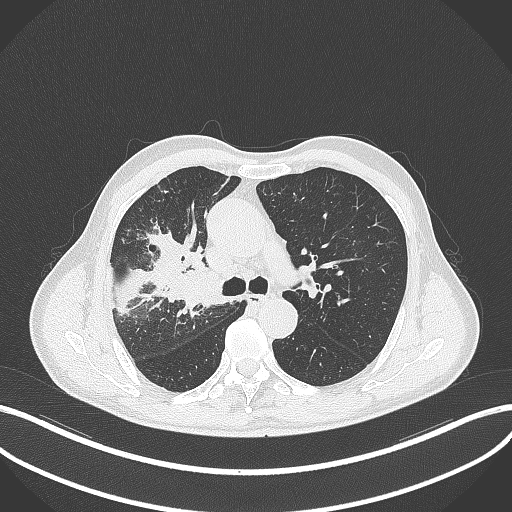
Chest CT, one axial slice. Position 321 of 490 along the scan axis. Reconstruction kernel B70f. 120 kVp. Lung window (W 1500 / L -600 HU). 1 mm slice thickness. 512 × 512 image matrix, field of view 400 × 400 mm. Male patient, age 69 years. From the clinical record (not read from this slice): clinical TNM (as recorded): T2a N0 M0.
Structures marked on this image (rectangle marked by the reading radiologist):
- lung tumour (recorded histology: adenocarcinoma): box from (x=165, y=257) to (x=224, y=314) px